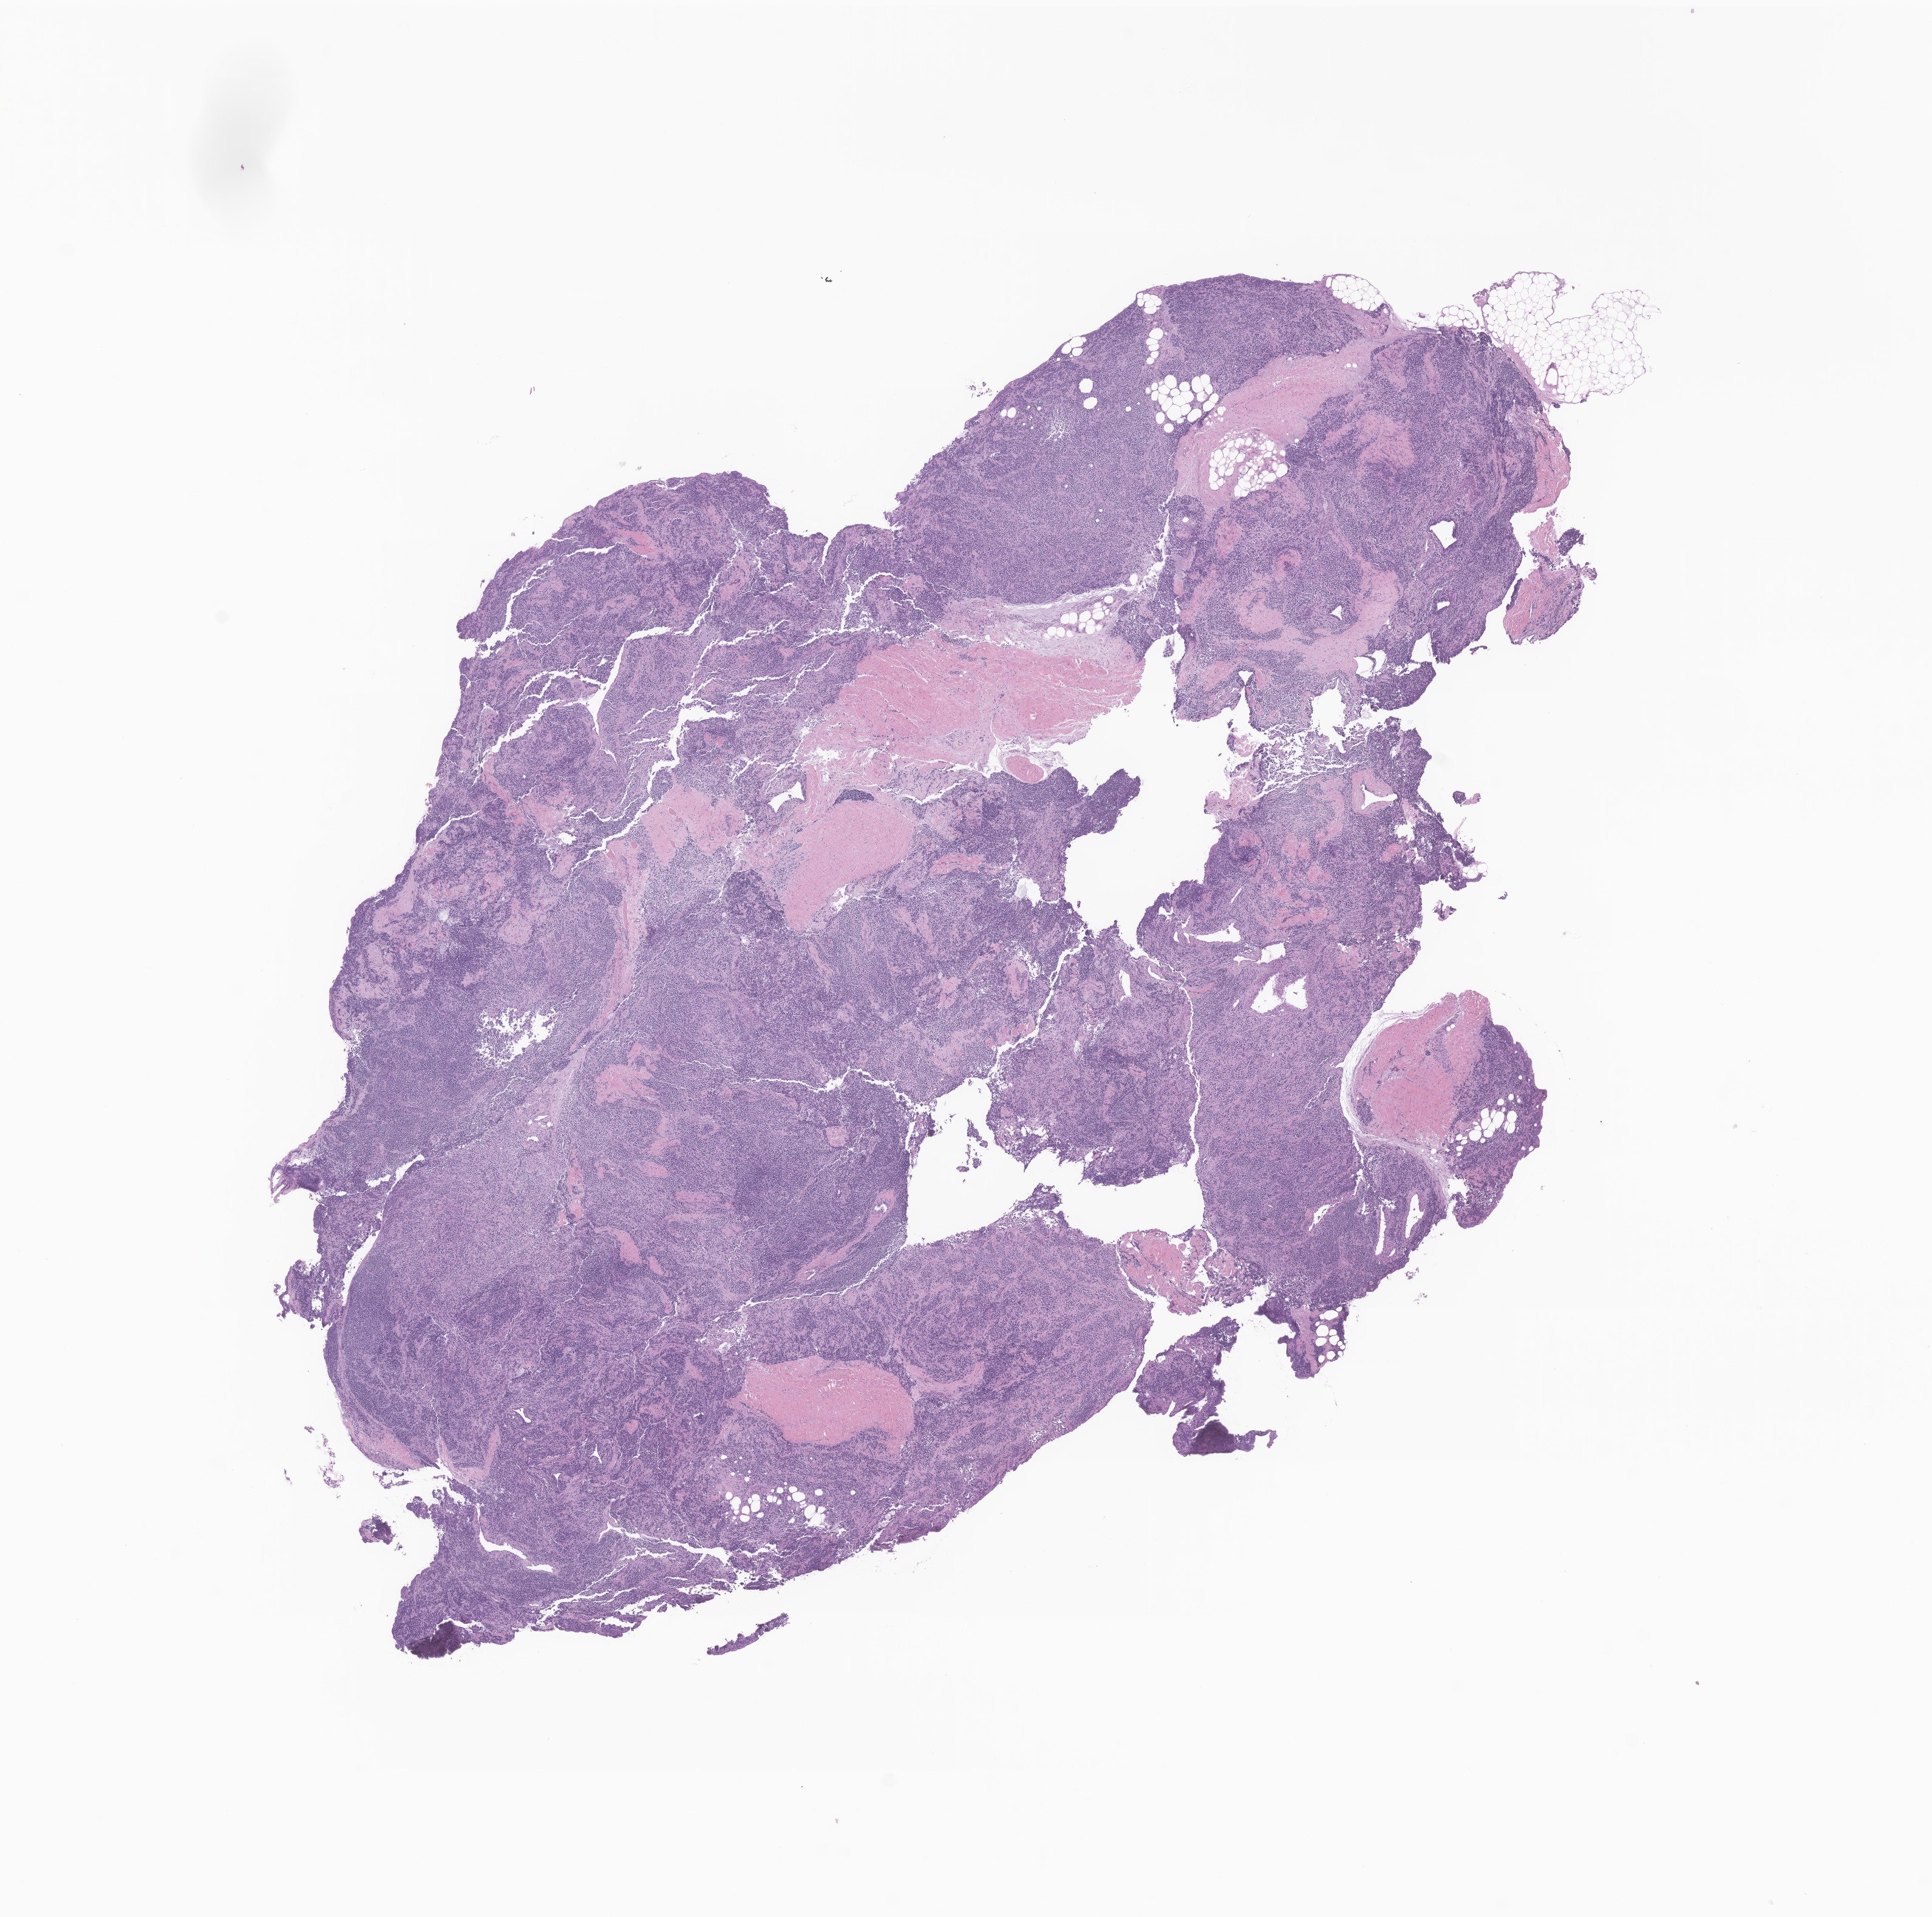
Whole-slide image, haematoxylin and eosin stain of tumor tissue from the soft tissue of lower extremity, whole scanned area (about 13.4 x 13.3 mm) shown as a low-resolution overview; formalin-fixed, paraffin-embedded (FFPE) tissue. Patient female; age 121 months (10 years 1 month).
• diagnosis: Alveolar rhabdomyosarcoma